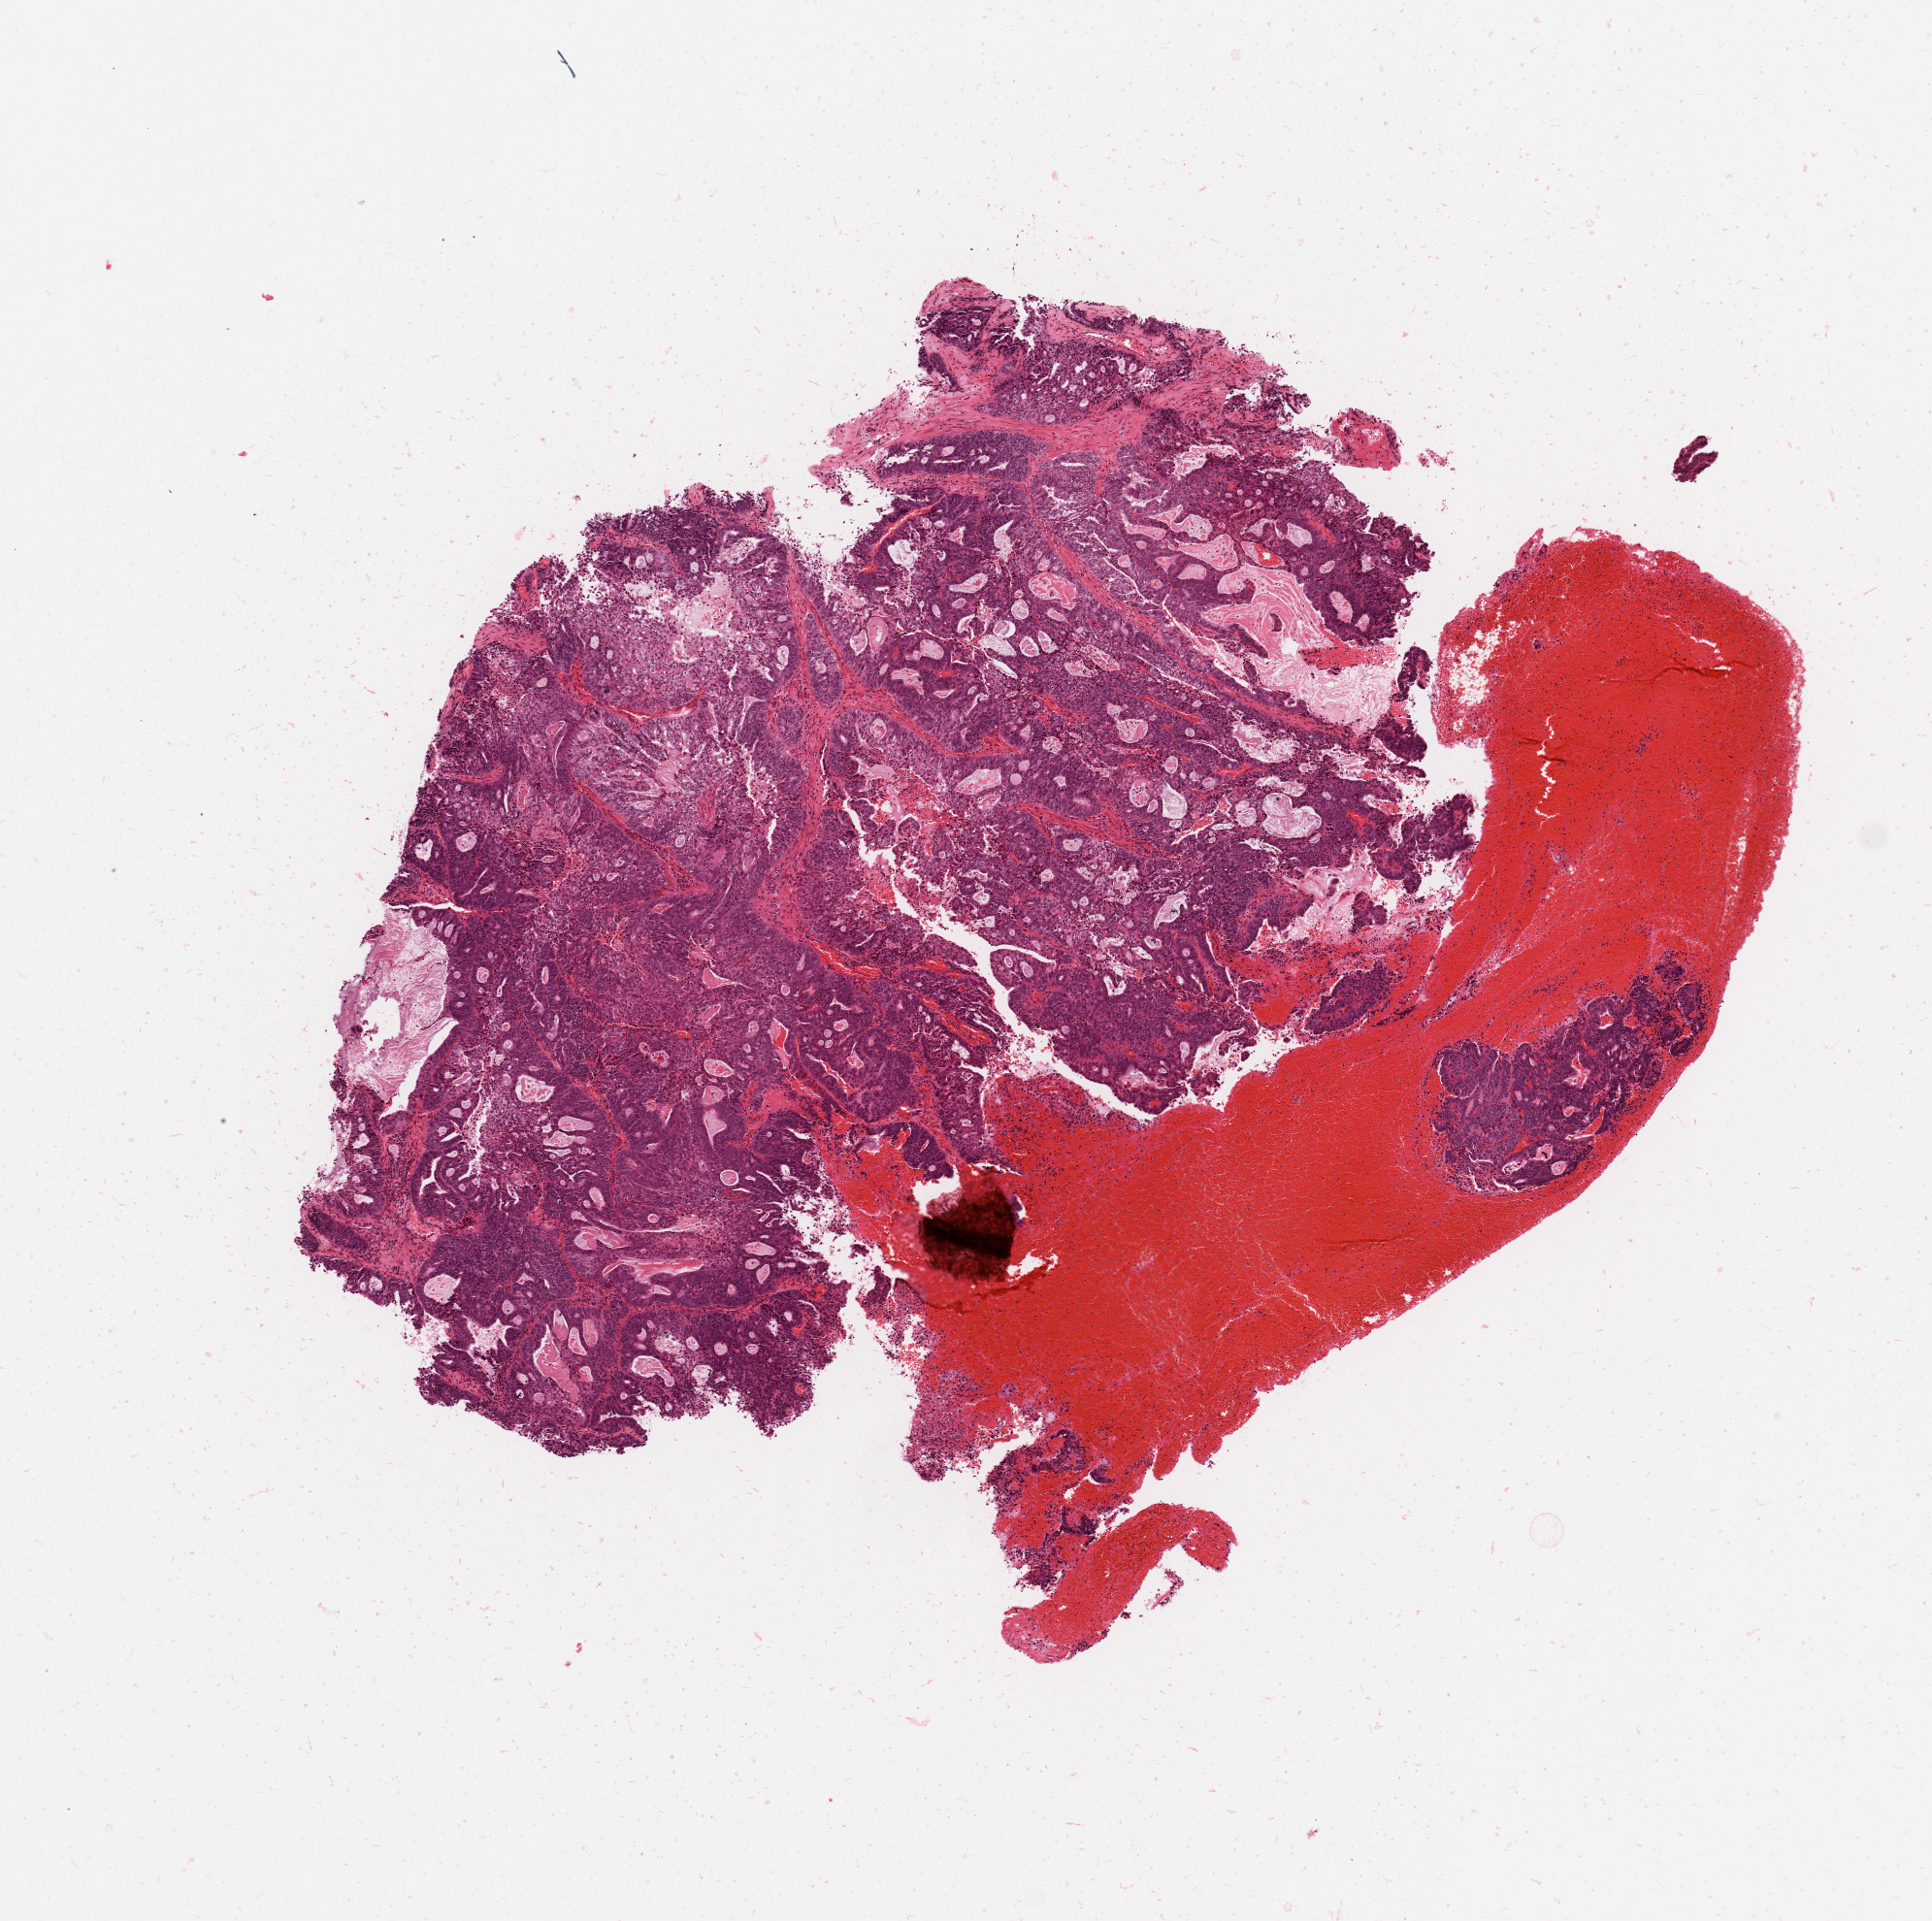
Digitized Hematoxylin and eosin (H&E) stained tissue section (whole slide) — shown as a low-resolution overview of the whole scanned area (about 7.9 x 7.8 mm). Tumour tissue sample, sampled site: uterus. Female, 59 y/o.
Histologic diagnosis: Endometrioid adenocarcinoma, NOS.